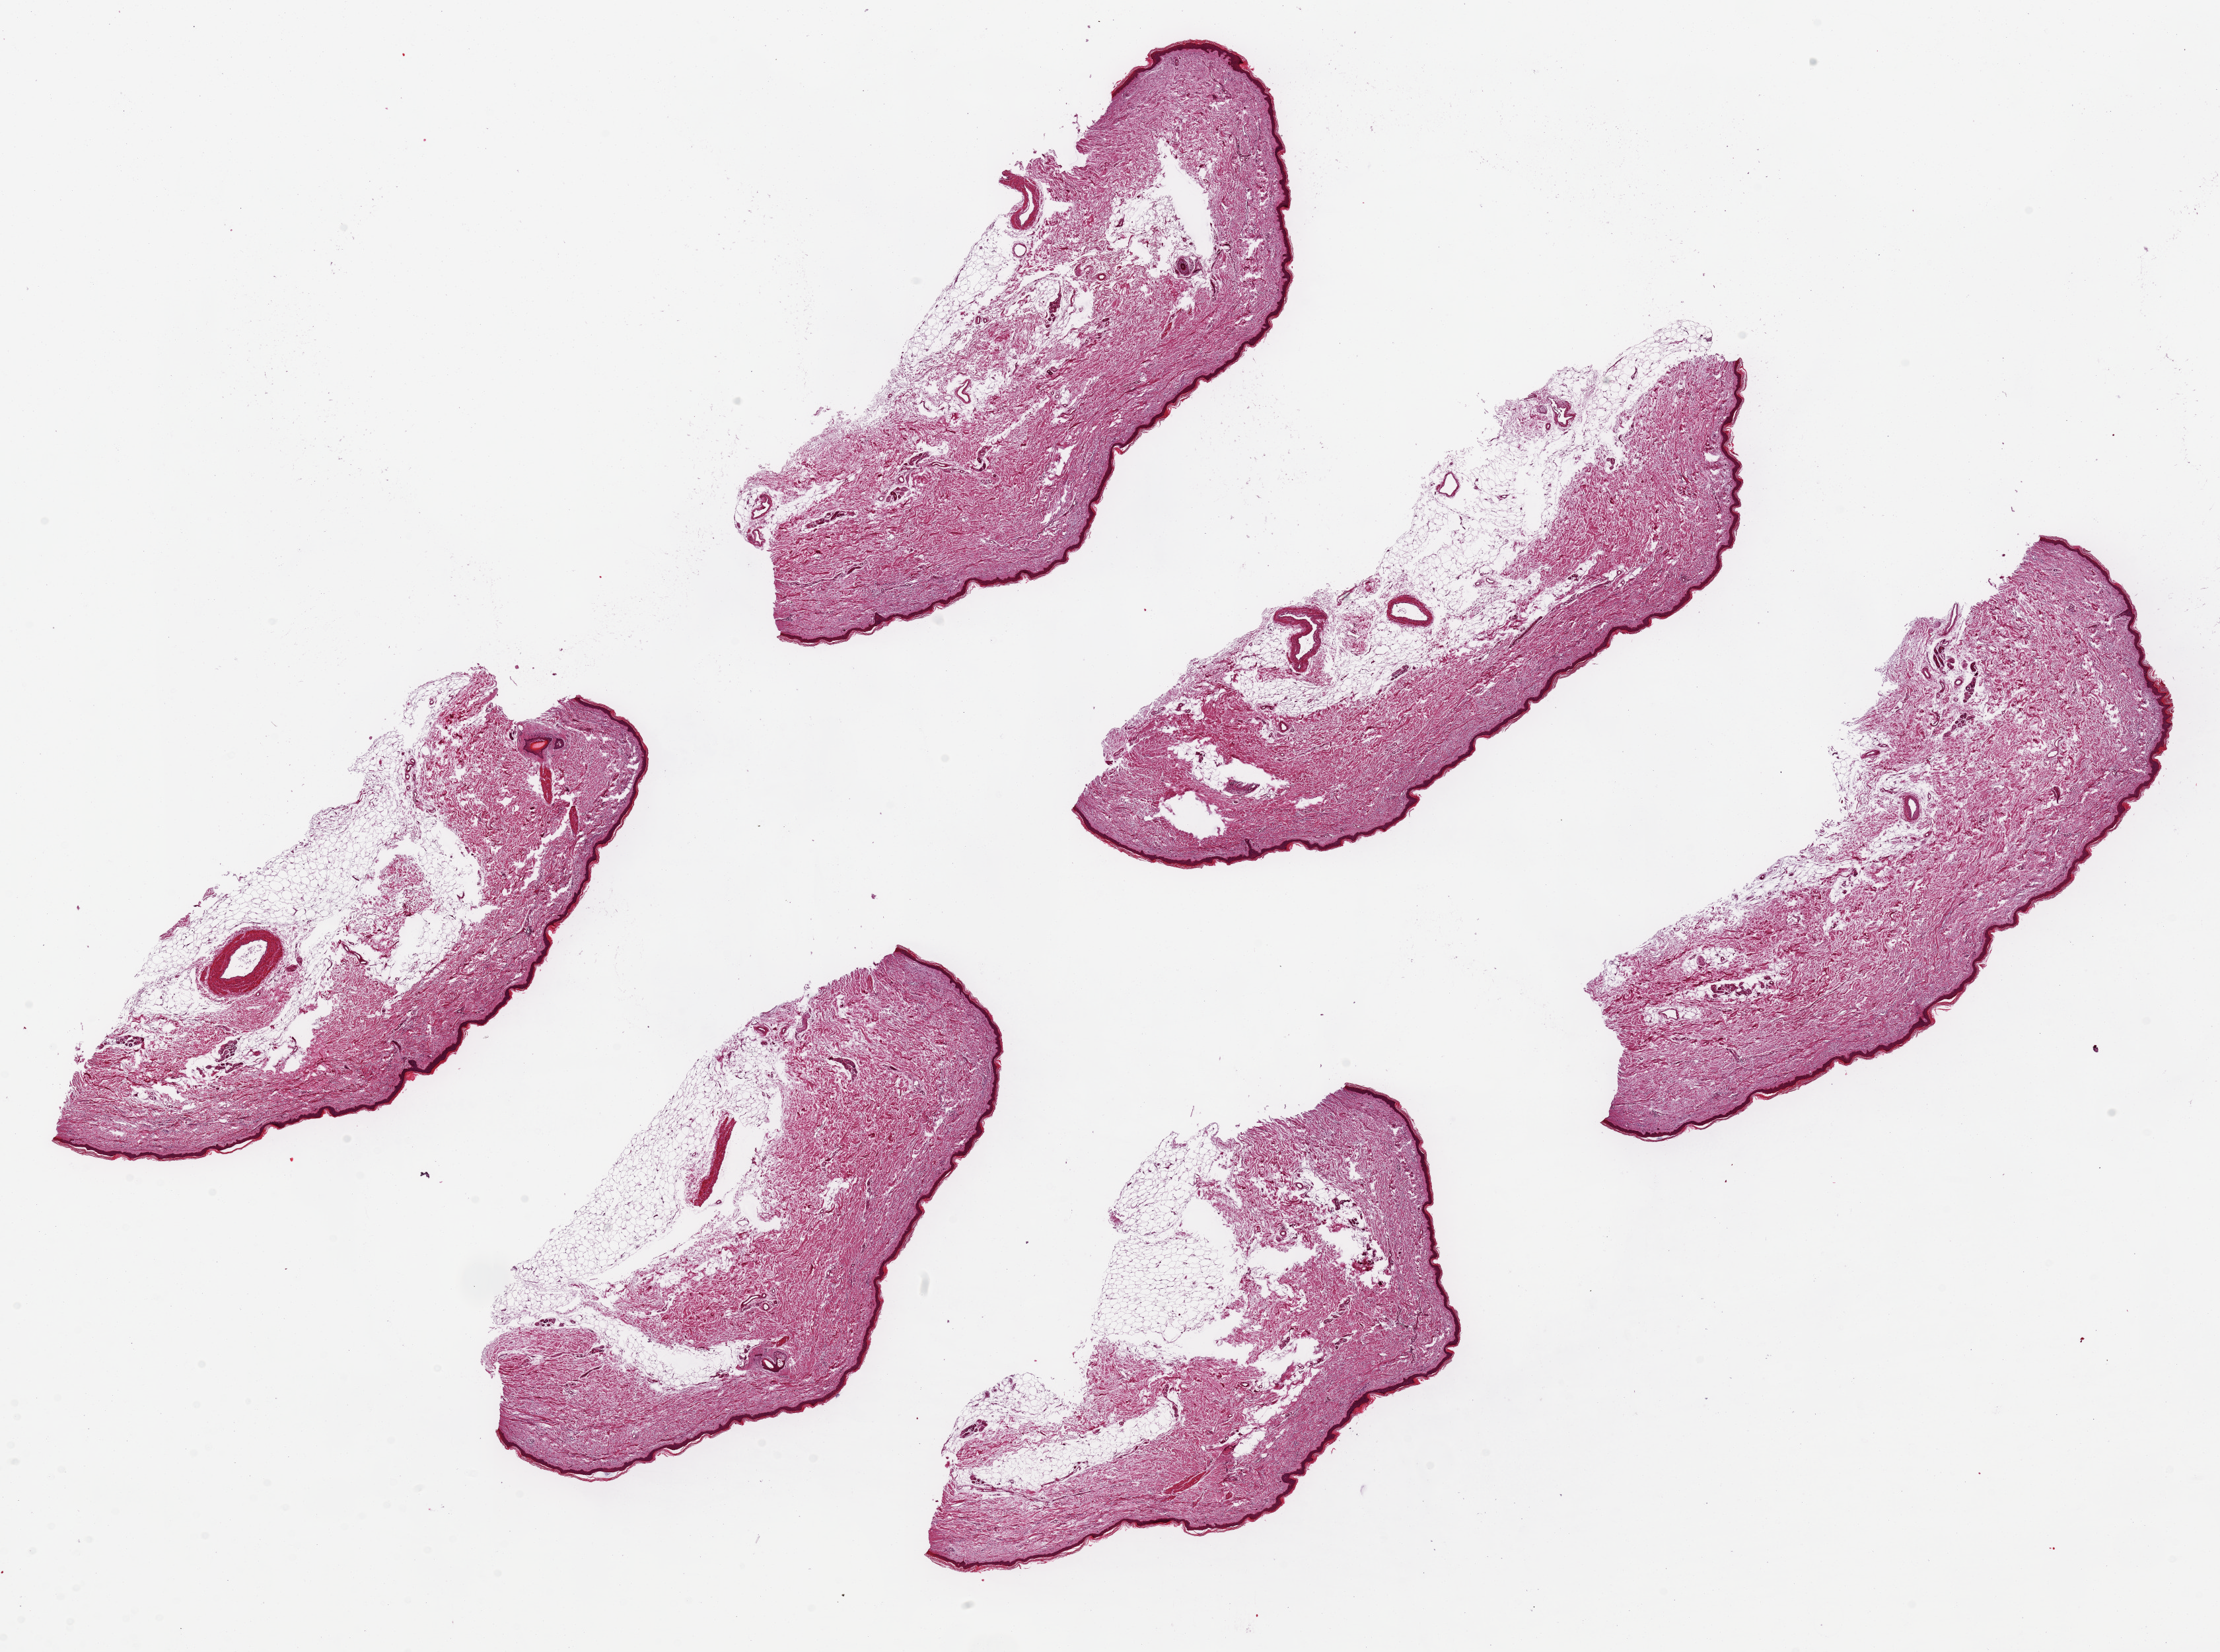
Digitized hematoxylin and eosin (H&E)-stained section — whole scanned area (about 26.6 x 19.8 mm) shown as a low-resolution overview; PAXgene-fixed, paraffin-embedded tissue; sampled site (target tissue): skin of lower leg; tissue donor sample. Female donor.
Pathologist's review note for this sample: 6 pieces, up to 9x3.6 mm.